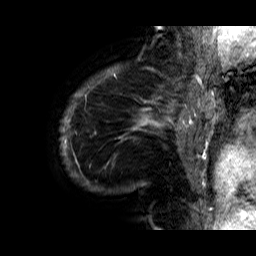
Breast MRI (dynamic contrast-enhanced), one sagittal slice; slice 2 of 60 in the series (ordered by position); dynamic contrast-enhanced series, time point 2 of 6 at this slice position (early post-contrast); 1.5 T; TE 6.3 ms, TR 32.9 ms; 4 mm slice thickness; 256 × 256 image matrix, field of view 200 × 200 mm. Female patient. Case-level facts recorded for this patient, not image findings: setting: breast cancer imaged before/during neoadjuvant chemotherapy; receptor status: HR-positive, HER2-negative.
Outlined on this slice (semi-automatic segmentation, software-assisted and operator-edited):
- analysis volume of interest (the breast-tissue region the enhancement analysis was run in; not a lesion): box from (x=59, y=74) to (x=176, y=200) px
- tumour enhancement mask (voxels above the 100 % enhancement threshold inside the analysis volume of interest): (x=60, y=74)–(x=175, y=185)